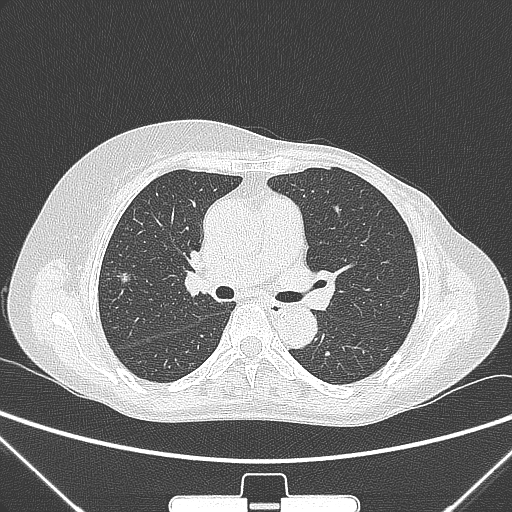
Chest CT, one axial slice; position 151 of 265 along the scan axis; 120 kVp; lung window (W 1500 / L -600 HU); 1 mm slice thickness; 512 × 512 image matrix, field of view 350 × 350 mm. Patient: female, 64 years. Case-level facts recorded for this patient, not image findings: clinical TNM (as recorded): T1c N0 M0; histopathological grade: G1-2.
Outlined on this slice (bounding box drawn by a radiologist):
- lung tumour (recorded histology: adenocarcinoma): bounding box [x1, y1, x2, y2] px = [114, 265, 134, 292]